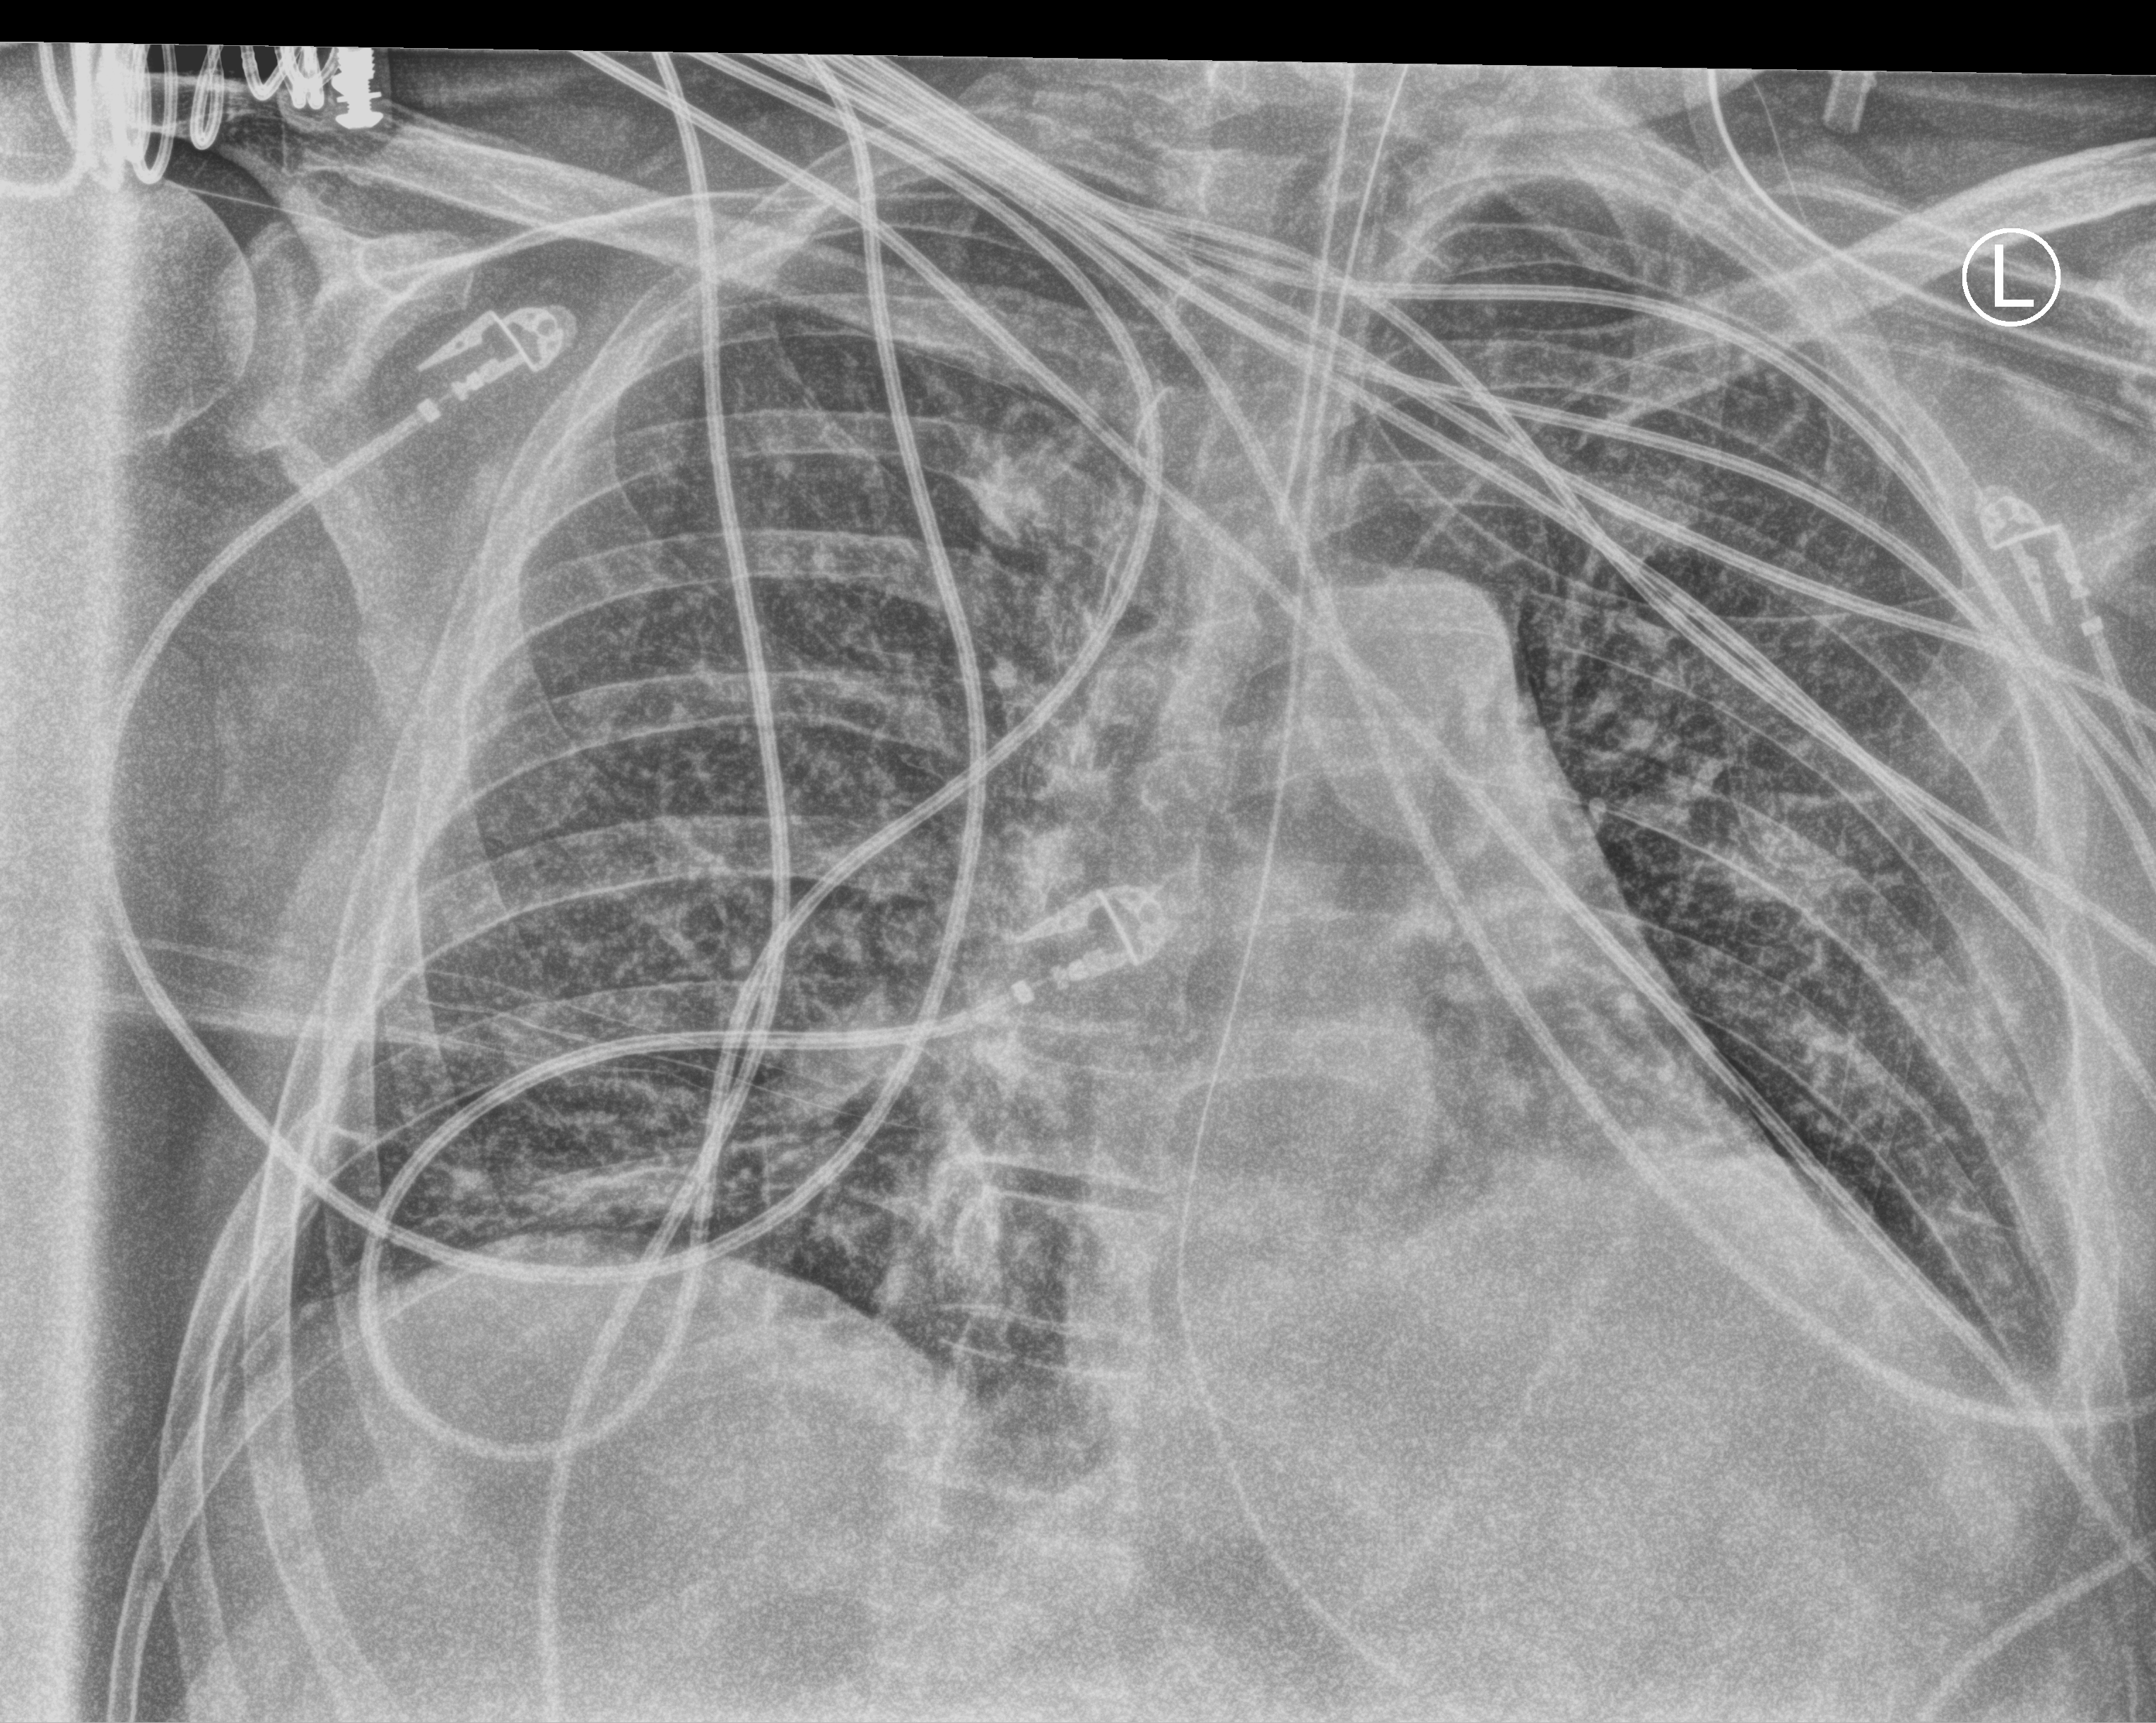
Bedside chest radiograph (computed radiography). Male patient hospitalised with COVID-19, age 60–74 years.
From the hospital-stay record, not from the radiograph (when in the stay this image was taken is not recorded): admitted to intensive care during this hospital stay: yes; COPD (admission record): no; smoking status (admission record): never.